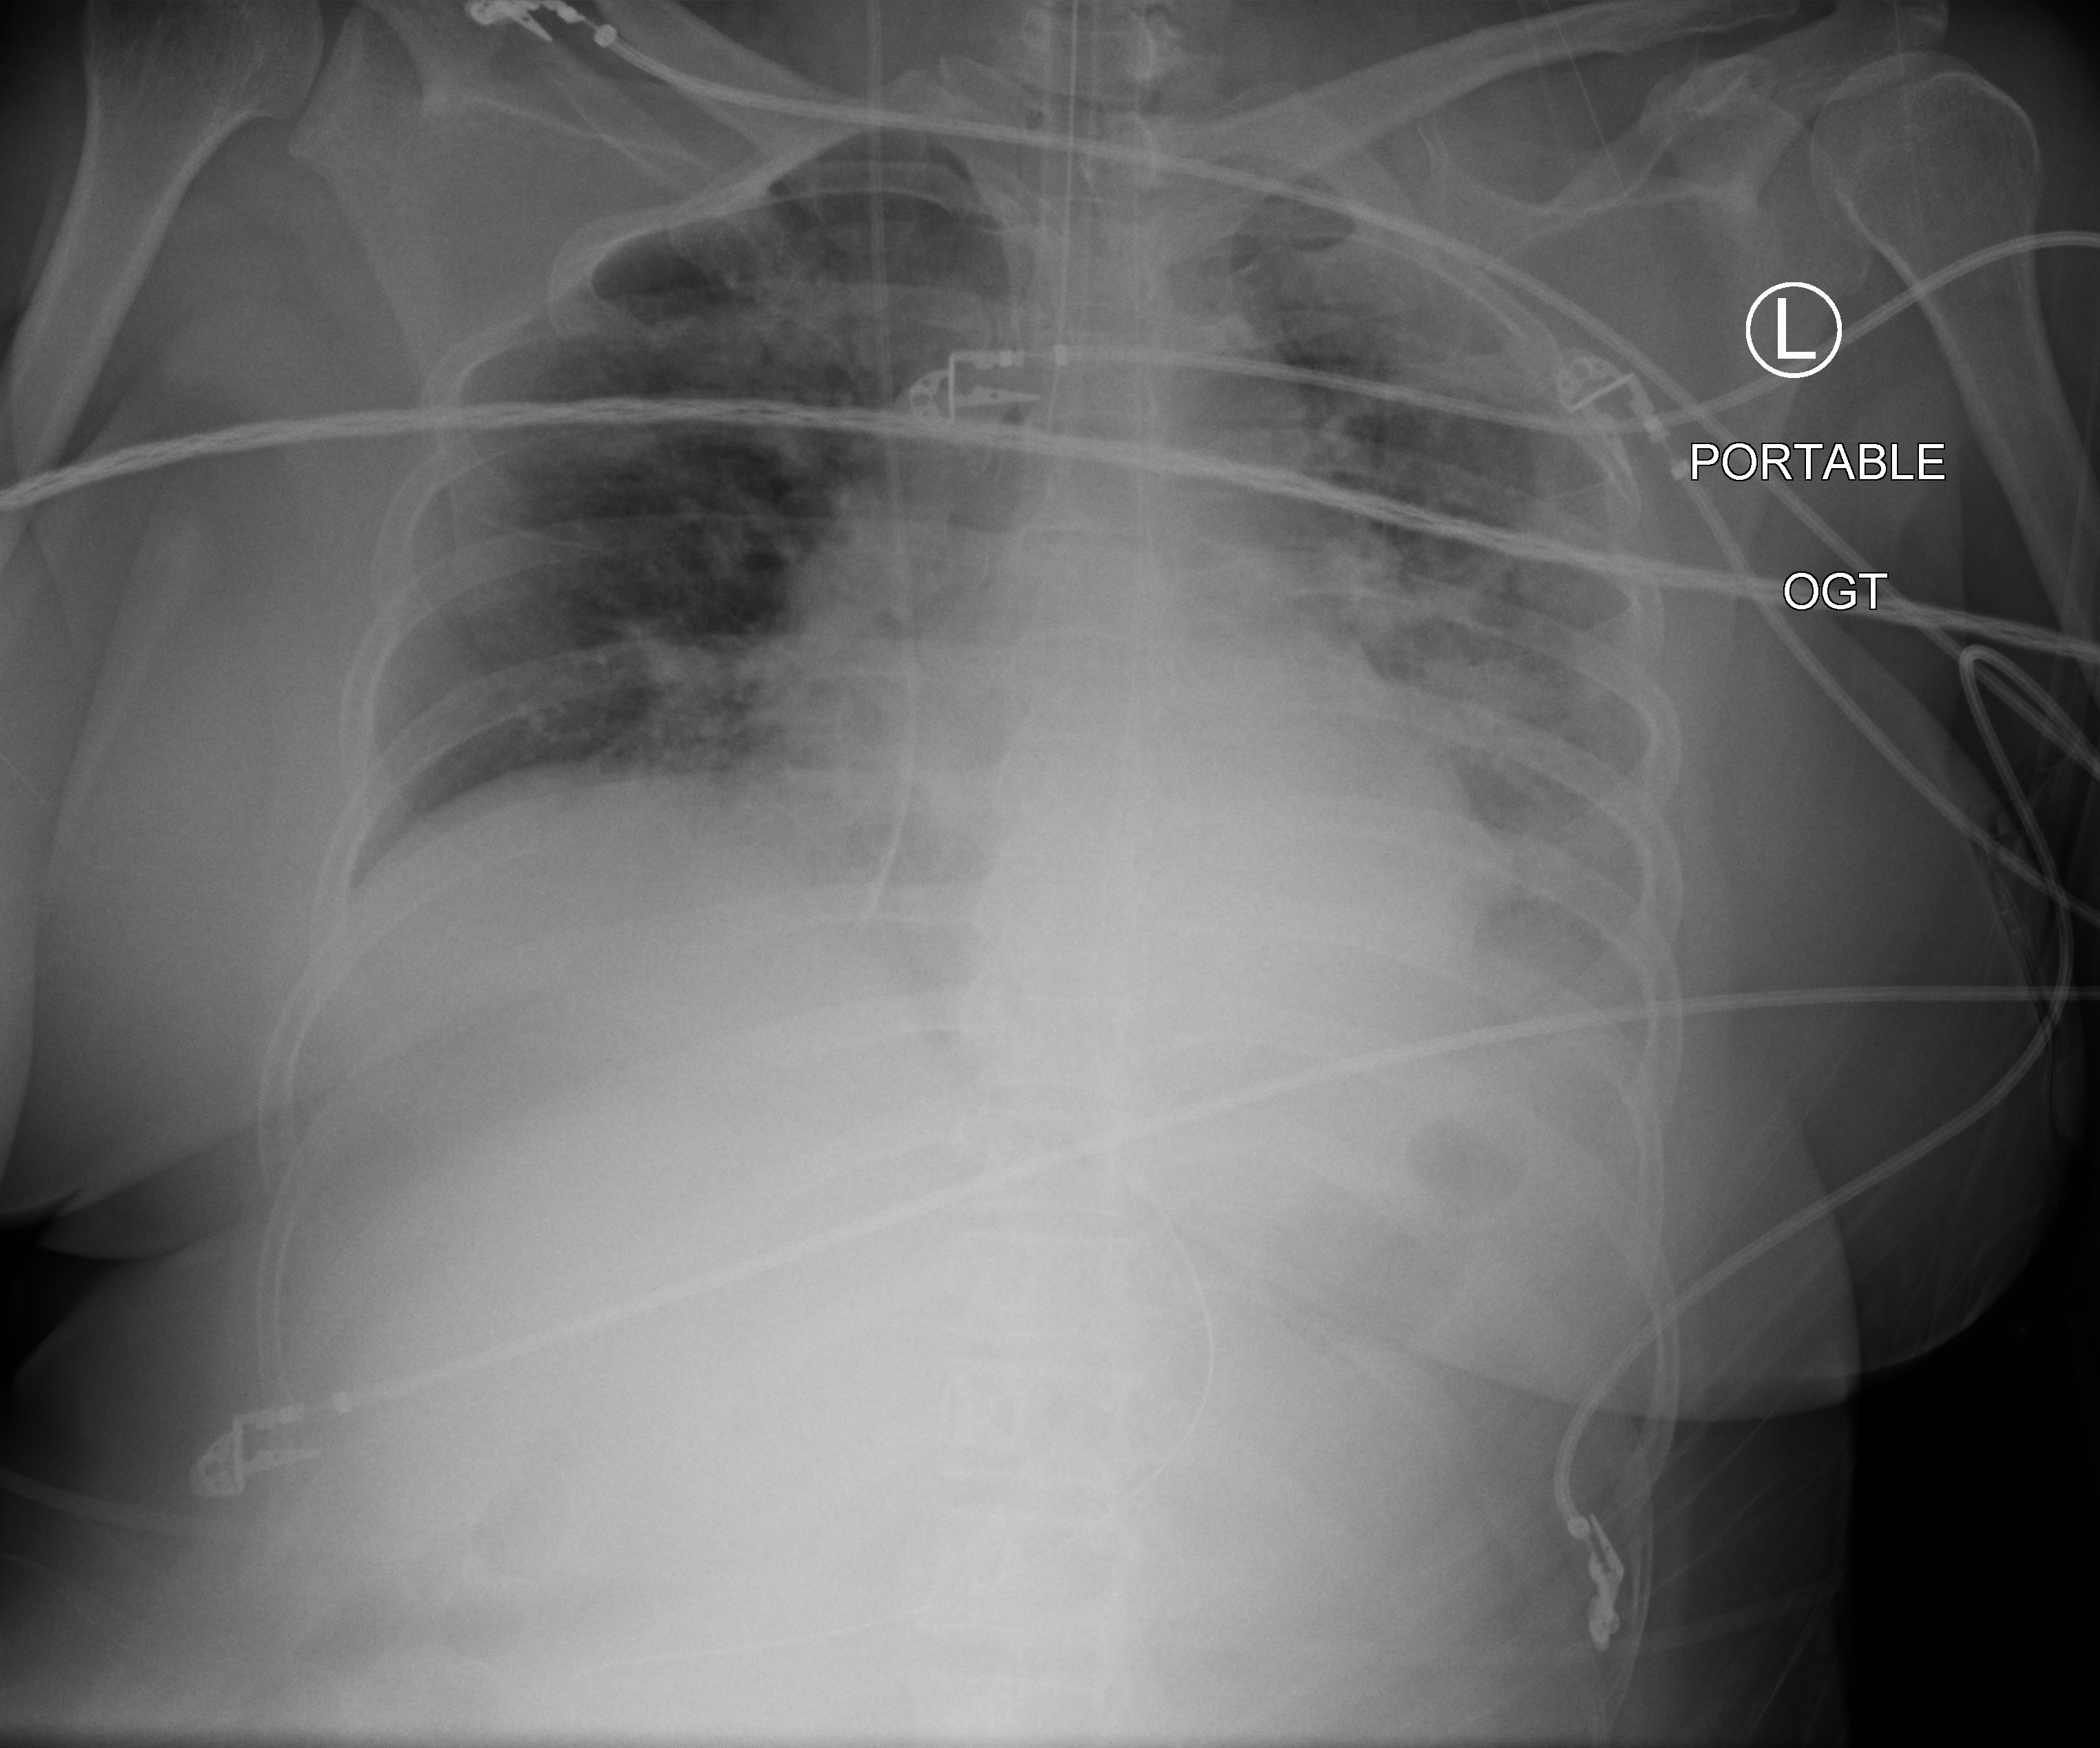
Portable chest radiograph; anteroposterior (AP) projection. Female patient hospitalised with COVID-19, age 18–59 years.
Admission-level facts for this patient (not findings on this image; timing relative to this image not recorded): other chronic lung disease (admission record): no; chronic kidney disease (admission record): no; admitted to intensive care during this hospital stay: yes.